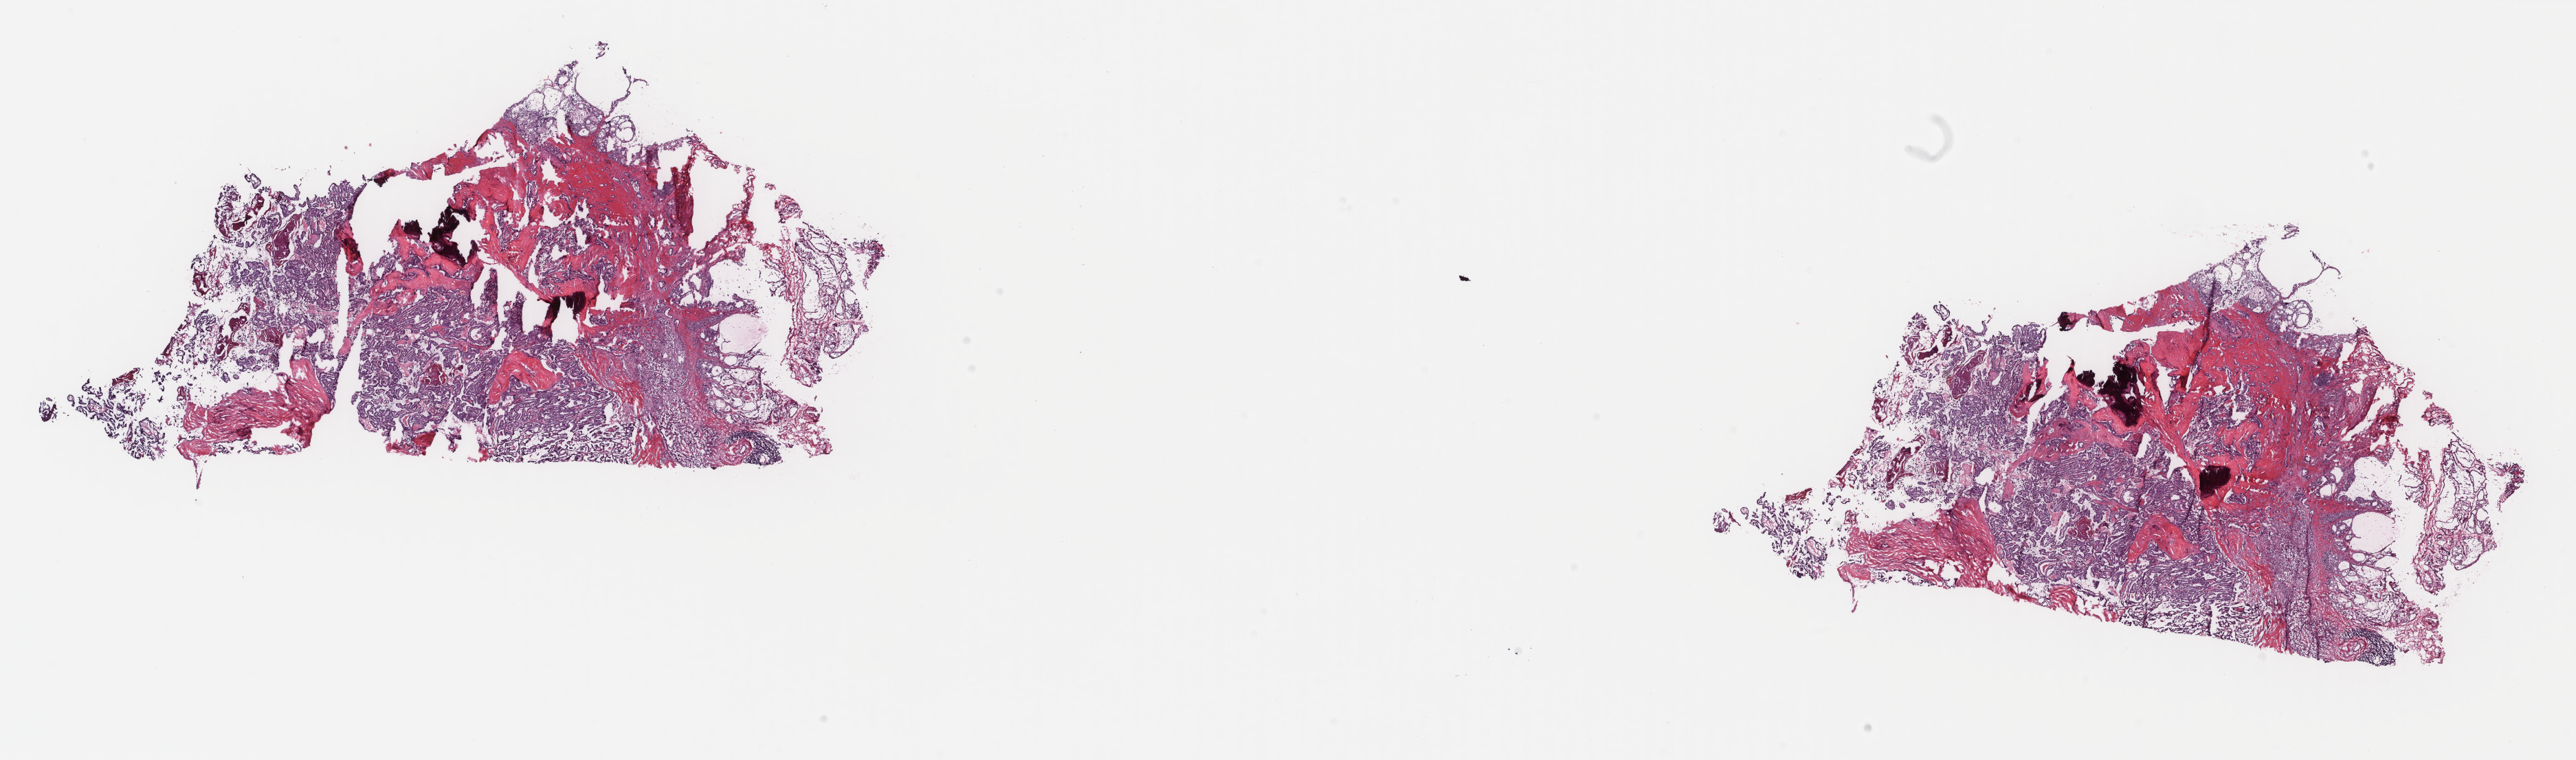
Digitized H&E-stained tissue section (whole slide), low-resolution overview of the scanned area, about 29.7 x 8.8 mm; frozen section from the top of the tissue portion; thyroid, primary tumour sample. Male, age 63 years at initial diagnosis. Pathologist review of this section (percent, as recorded): tumour cells 65%, tumour nuclei 65%, normal cells 20%, stromal cells 15%, necrosis 0%. Inflammatory infiltration, as recorded: lymphocyte infiltration 0%, monocyte infiltration 0%, neutrophil infiltration 0%.
Pathologic diagnosis: Papillary adenocarcinoma, NOS (thyroid gland). Laterality: left. AJCC pathologic stage: III (7th edition).